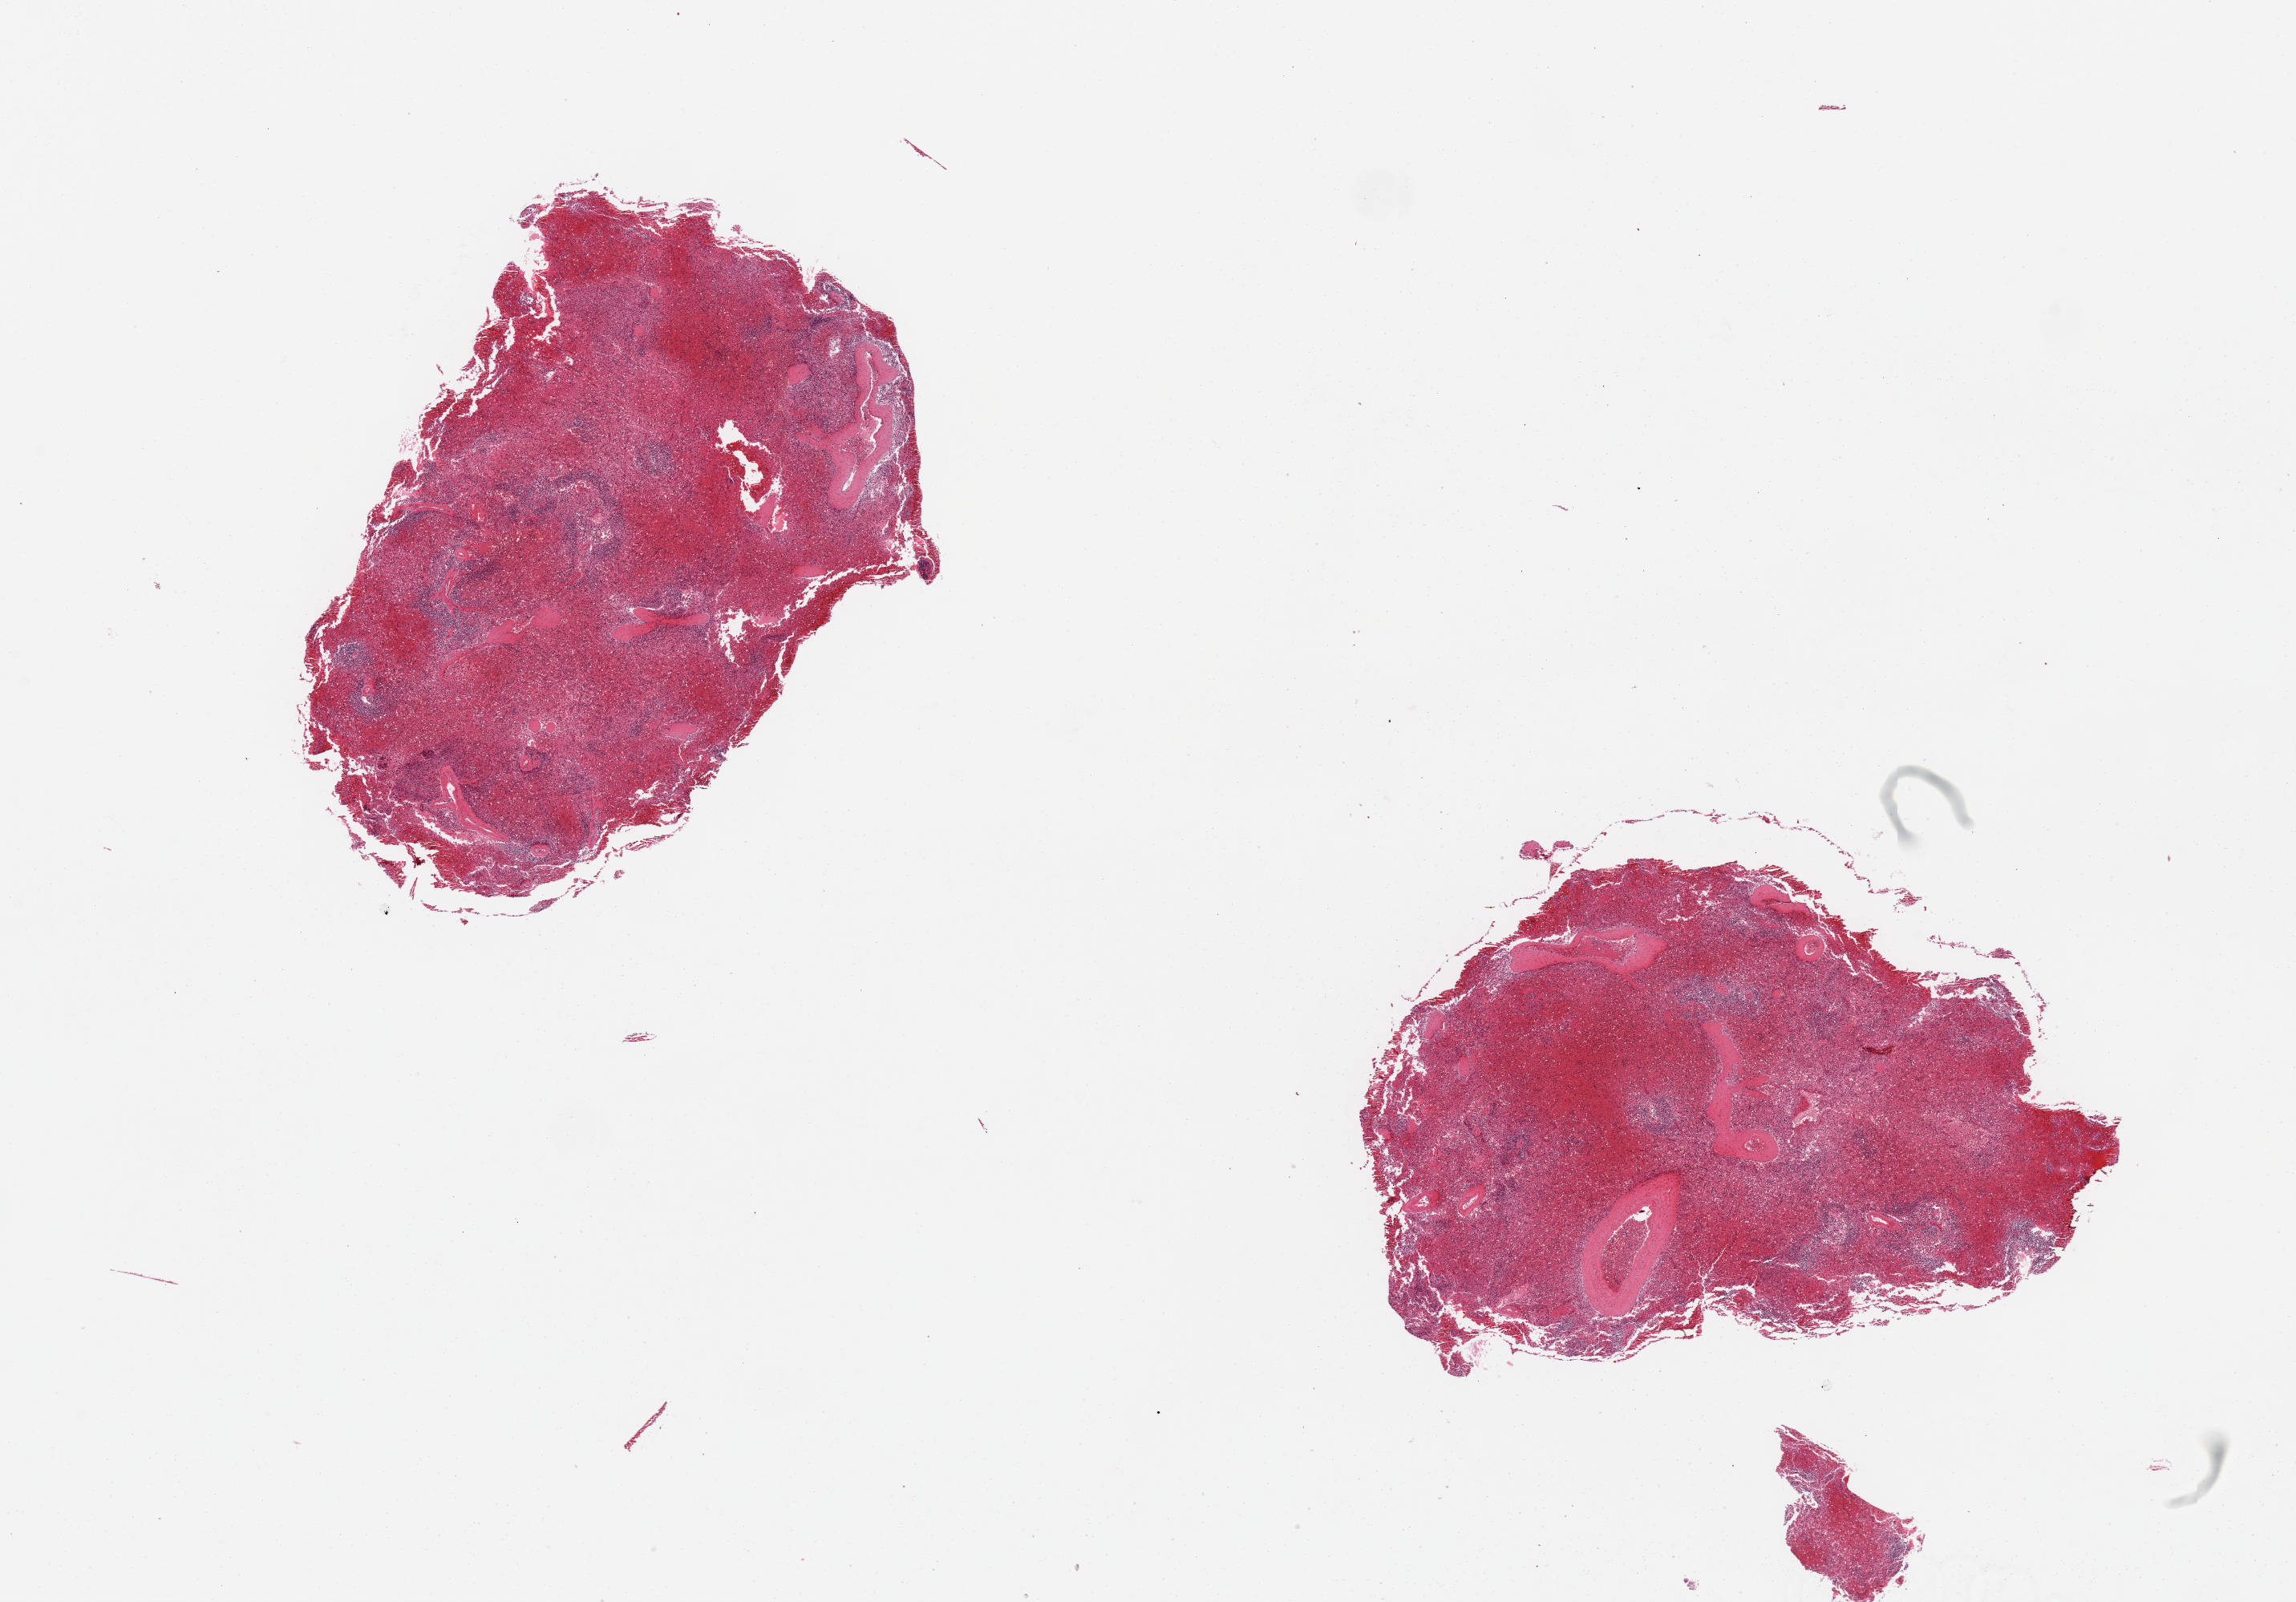
H&E whole-slide image, brightfield — shown as a low-resolution overview of the whole scanned area (about 22.6 x 15.8 mm, acquisition: 20x scan); PAXgene-fixed paraffin-embedded (PFPE) section; sampled site (target tissue): spleen; donor tissue sample. Donor sex: female.
- reviewer comment on this tissue sample: 2 pieces, marked congestion; badly autolyzed